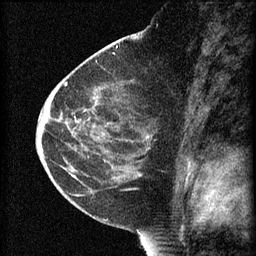
Breast MRI (dynamic contrast-enhanced), one sagittal slice. Slice 36 of 60 in the series (ordered by position). 3 images stored at this slice position (order not interpretable as contrast timing). 1.5 T. TE 4.2 ms, TR 8.2 ms. 2 mm slice thickness. 256 × 256 image matrix, field of view 180 × 180 mm. Female patient, age 44 years.
Structures marked on this image (semi-automatically segmented with operator editing):
- analysis volume of interest (the breast-tissue region the enhancement analysis was run in; not a lesion): bounding box [x1, y1, x2, y2] px = [73, 82, 158, 165]
- tumour enhancement mask (voxels above the 70 % enhancement threshold inside the analysis volume of interest): [75, 110, 150, 139]